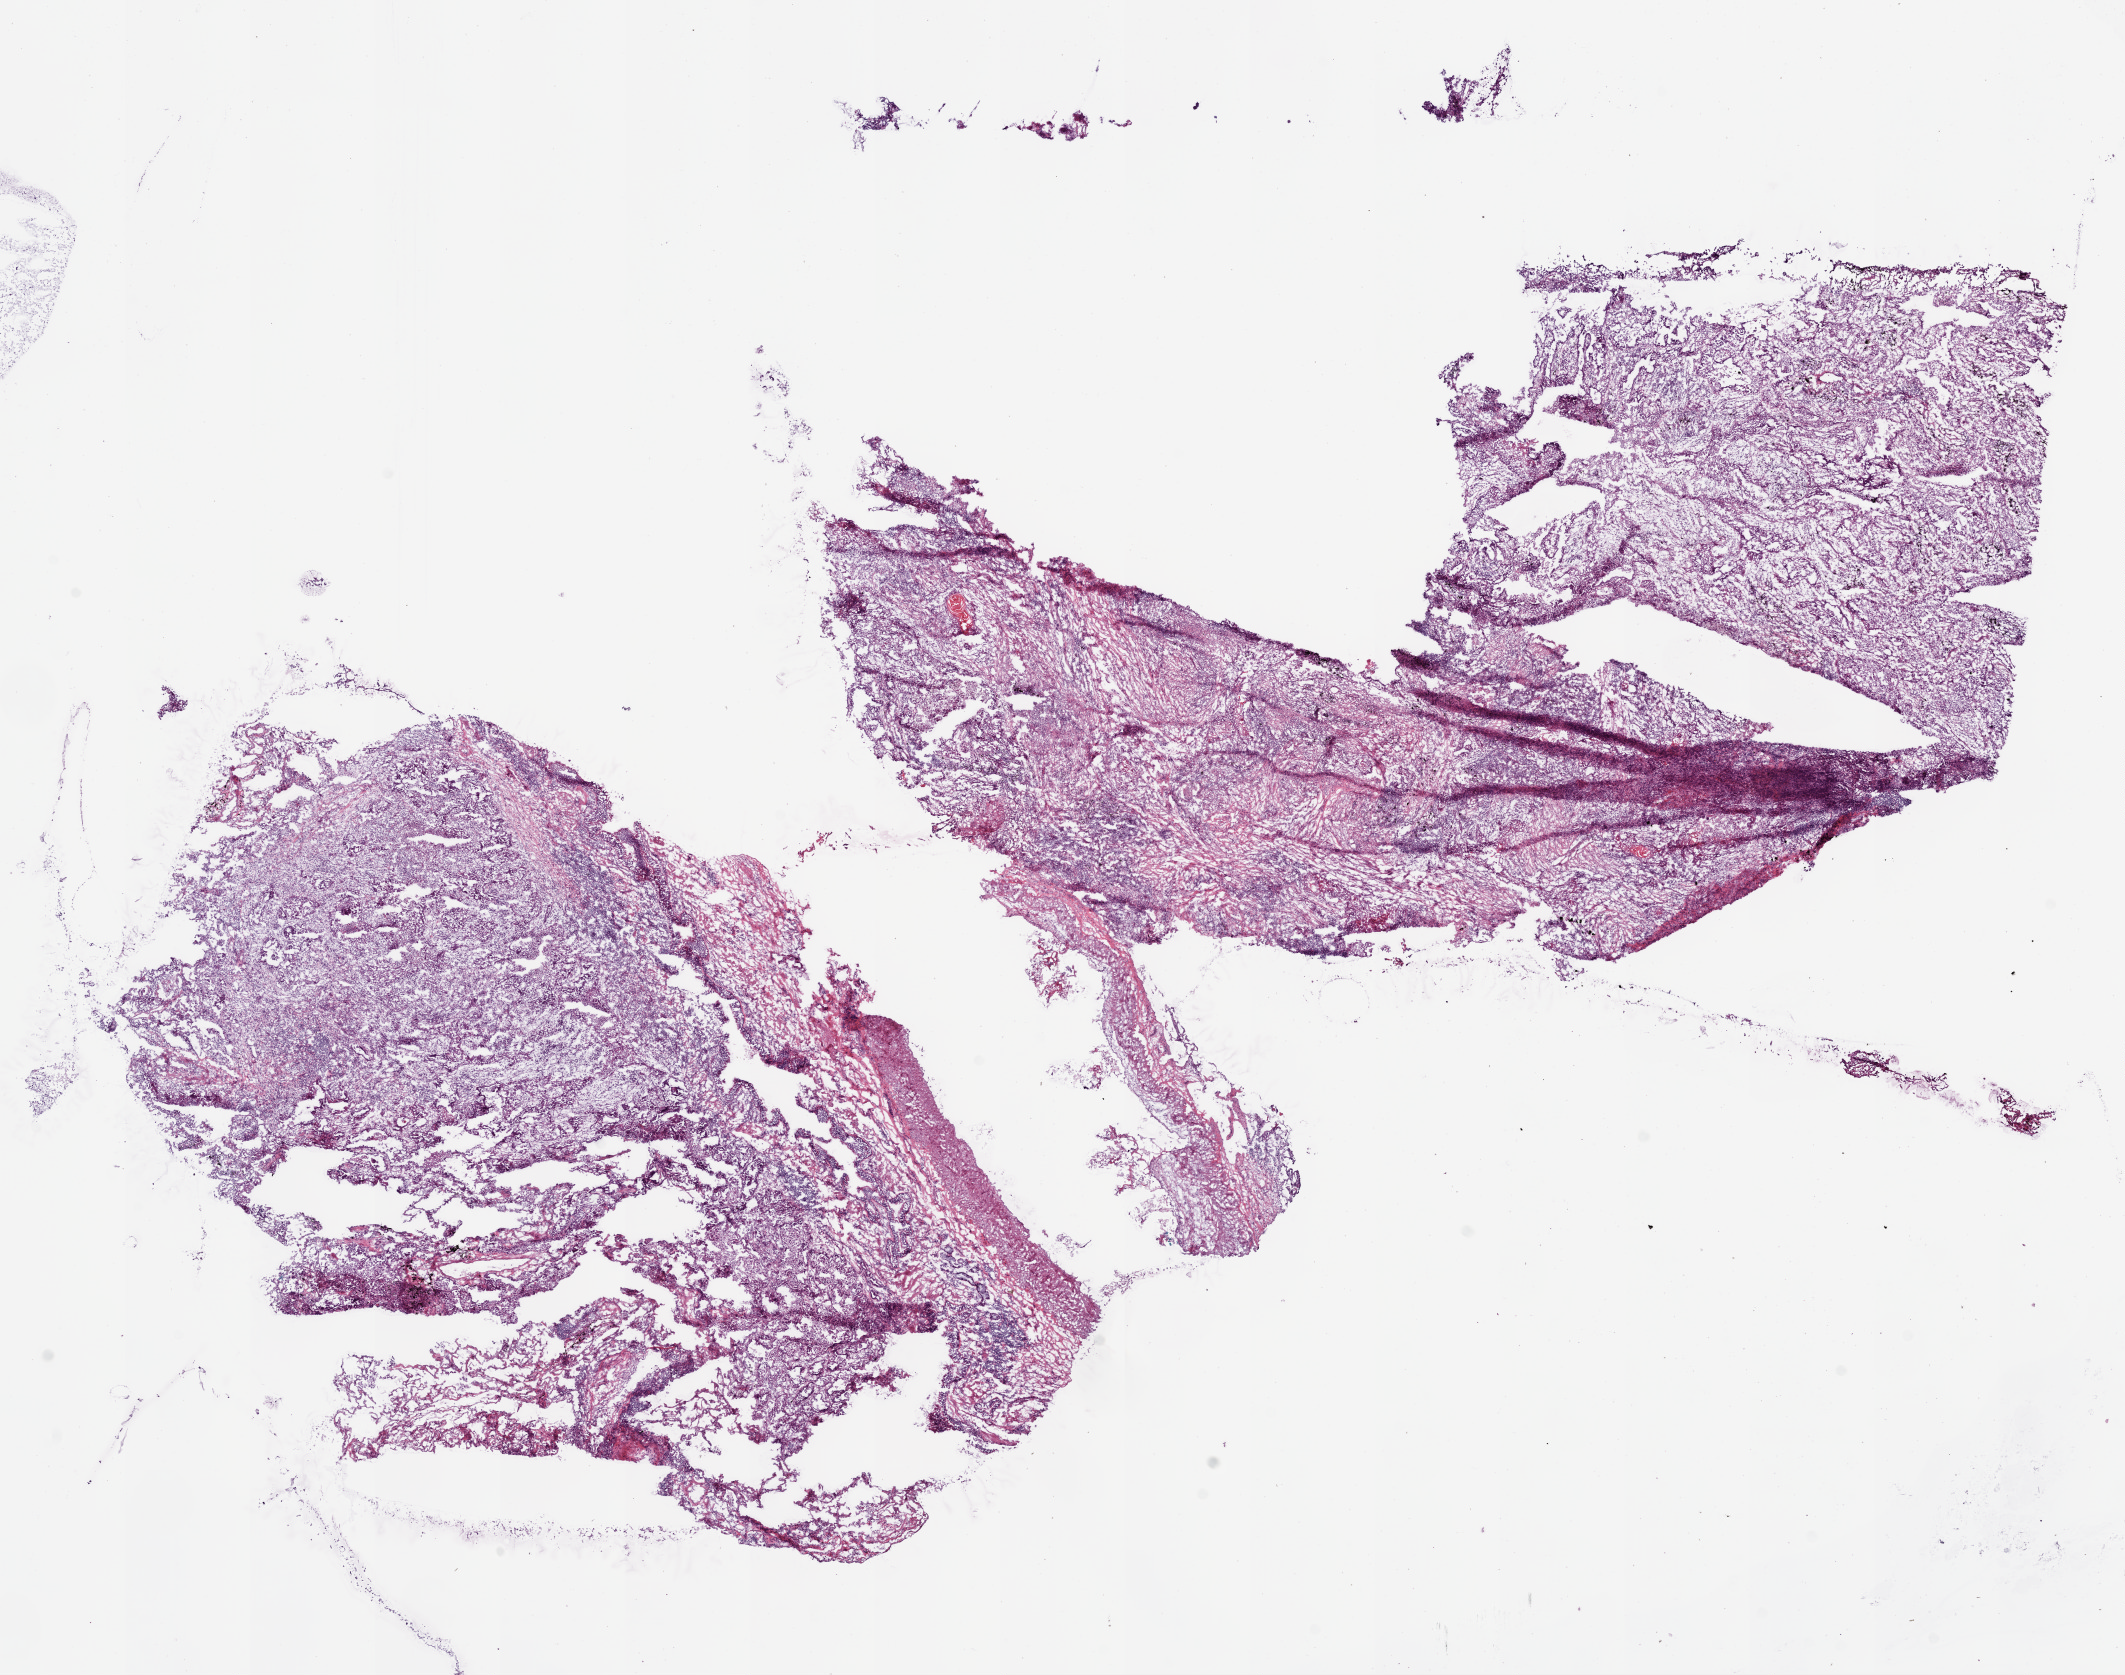
Hematoxylin and eosin (H&E) stained whole-slide image, a low-resolution overview of the entire scanned area, about 17.1 x 13.4 mm (slide scanned at 20x), frozen section from the bottom of the tissue portion, lung, primary tumour sample. Female, age 71 years at initial diagnosis. Pathologist review of this section (percent, as recorded): tumour cells 70%, tumour nuclei 50%, normal cells 10%, stromal cells 20%, necrosis 0%.
• diagnosis: Squamous cell carcinoma, NOS (upper lobe, lung)
• TNM: T1 N0 M0
• AJCC pathologic stage: IA (6th edition)